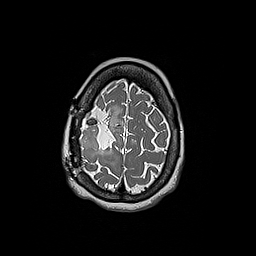
Brain MRI from a brain-tumour surgery series, one axial slice. Position 48 of 192 along the scan axis. 1 mm slice thickness. 256 × 256 image matrix. Case-level facts recorded for this patient, not image findings: histopathology: Oligodendroglioma; WHO grade: 3; IDH mutation: yes.
Structures marked on this image (outlined manually by an expert reader):
- tumour: bounding box <79,112,100,153> (left, top, right, bottom; pixels)